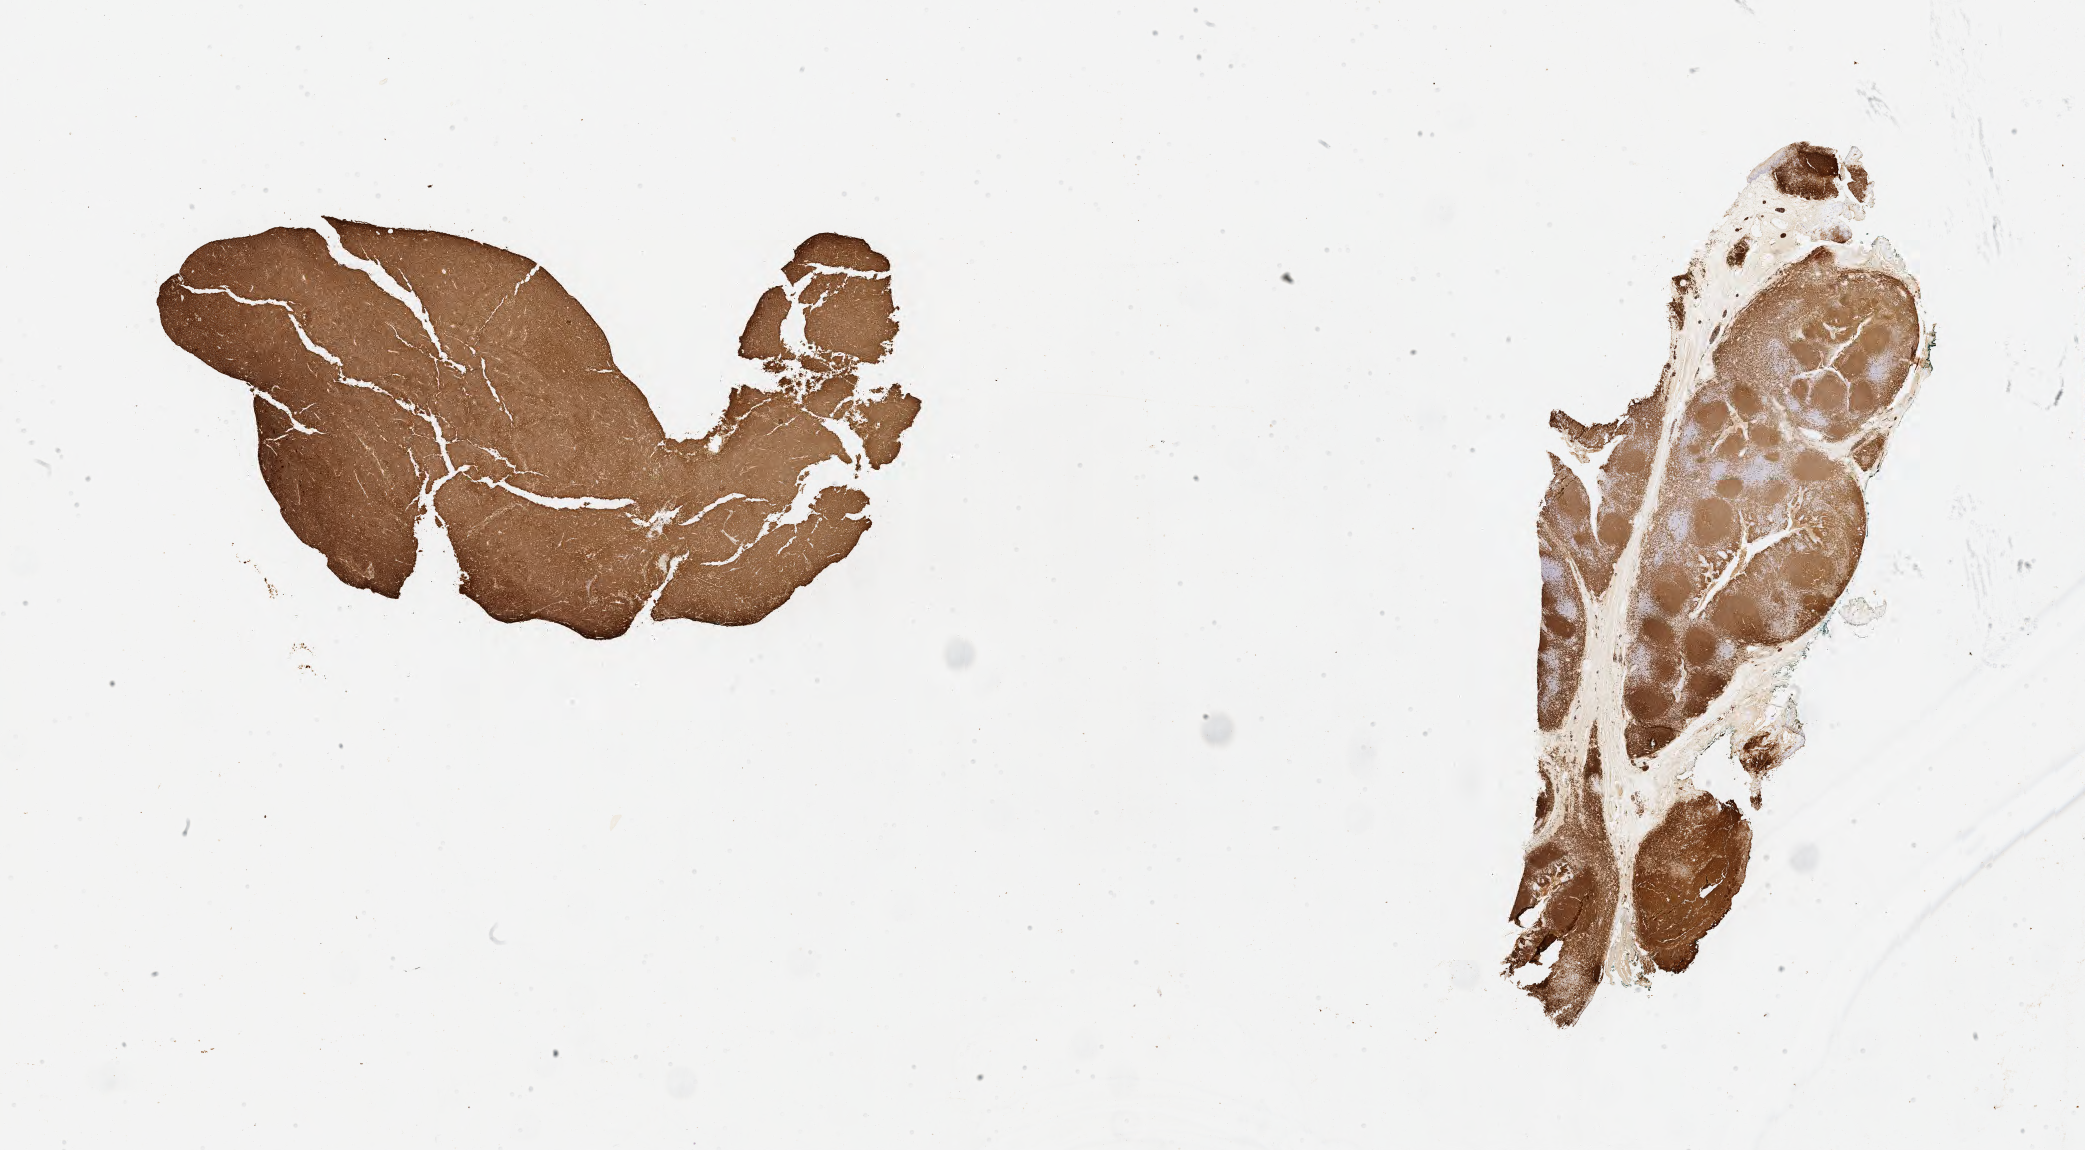
IHC for CD20, whole-slide image, a low-resolution overview of the entire scanned area, about 33.7 x 18.6 mm; tumor tissue; anatomic site: lymph node of head and neck. Male patient; age at initial diagnosis 5 years.
Histologic diagnosis: Burkitt lymphoma, NOS.